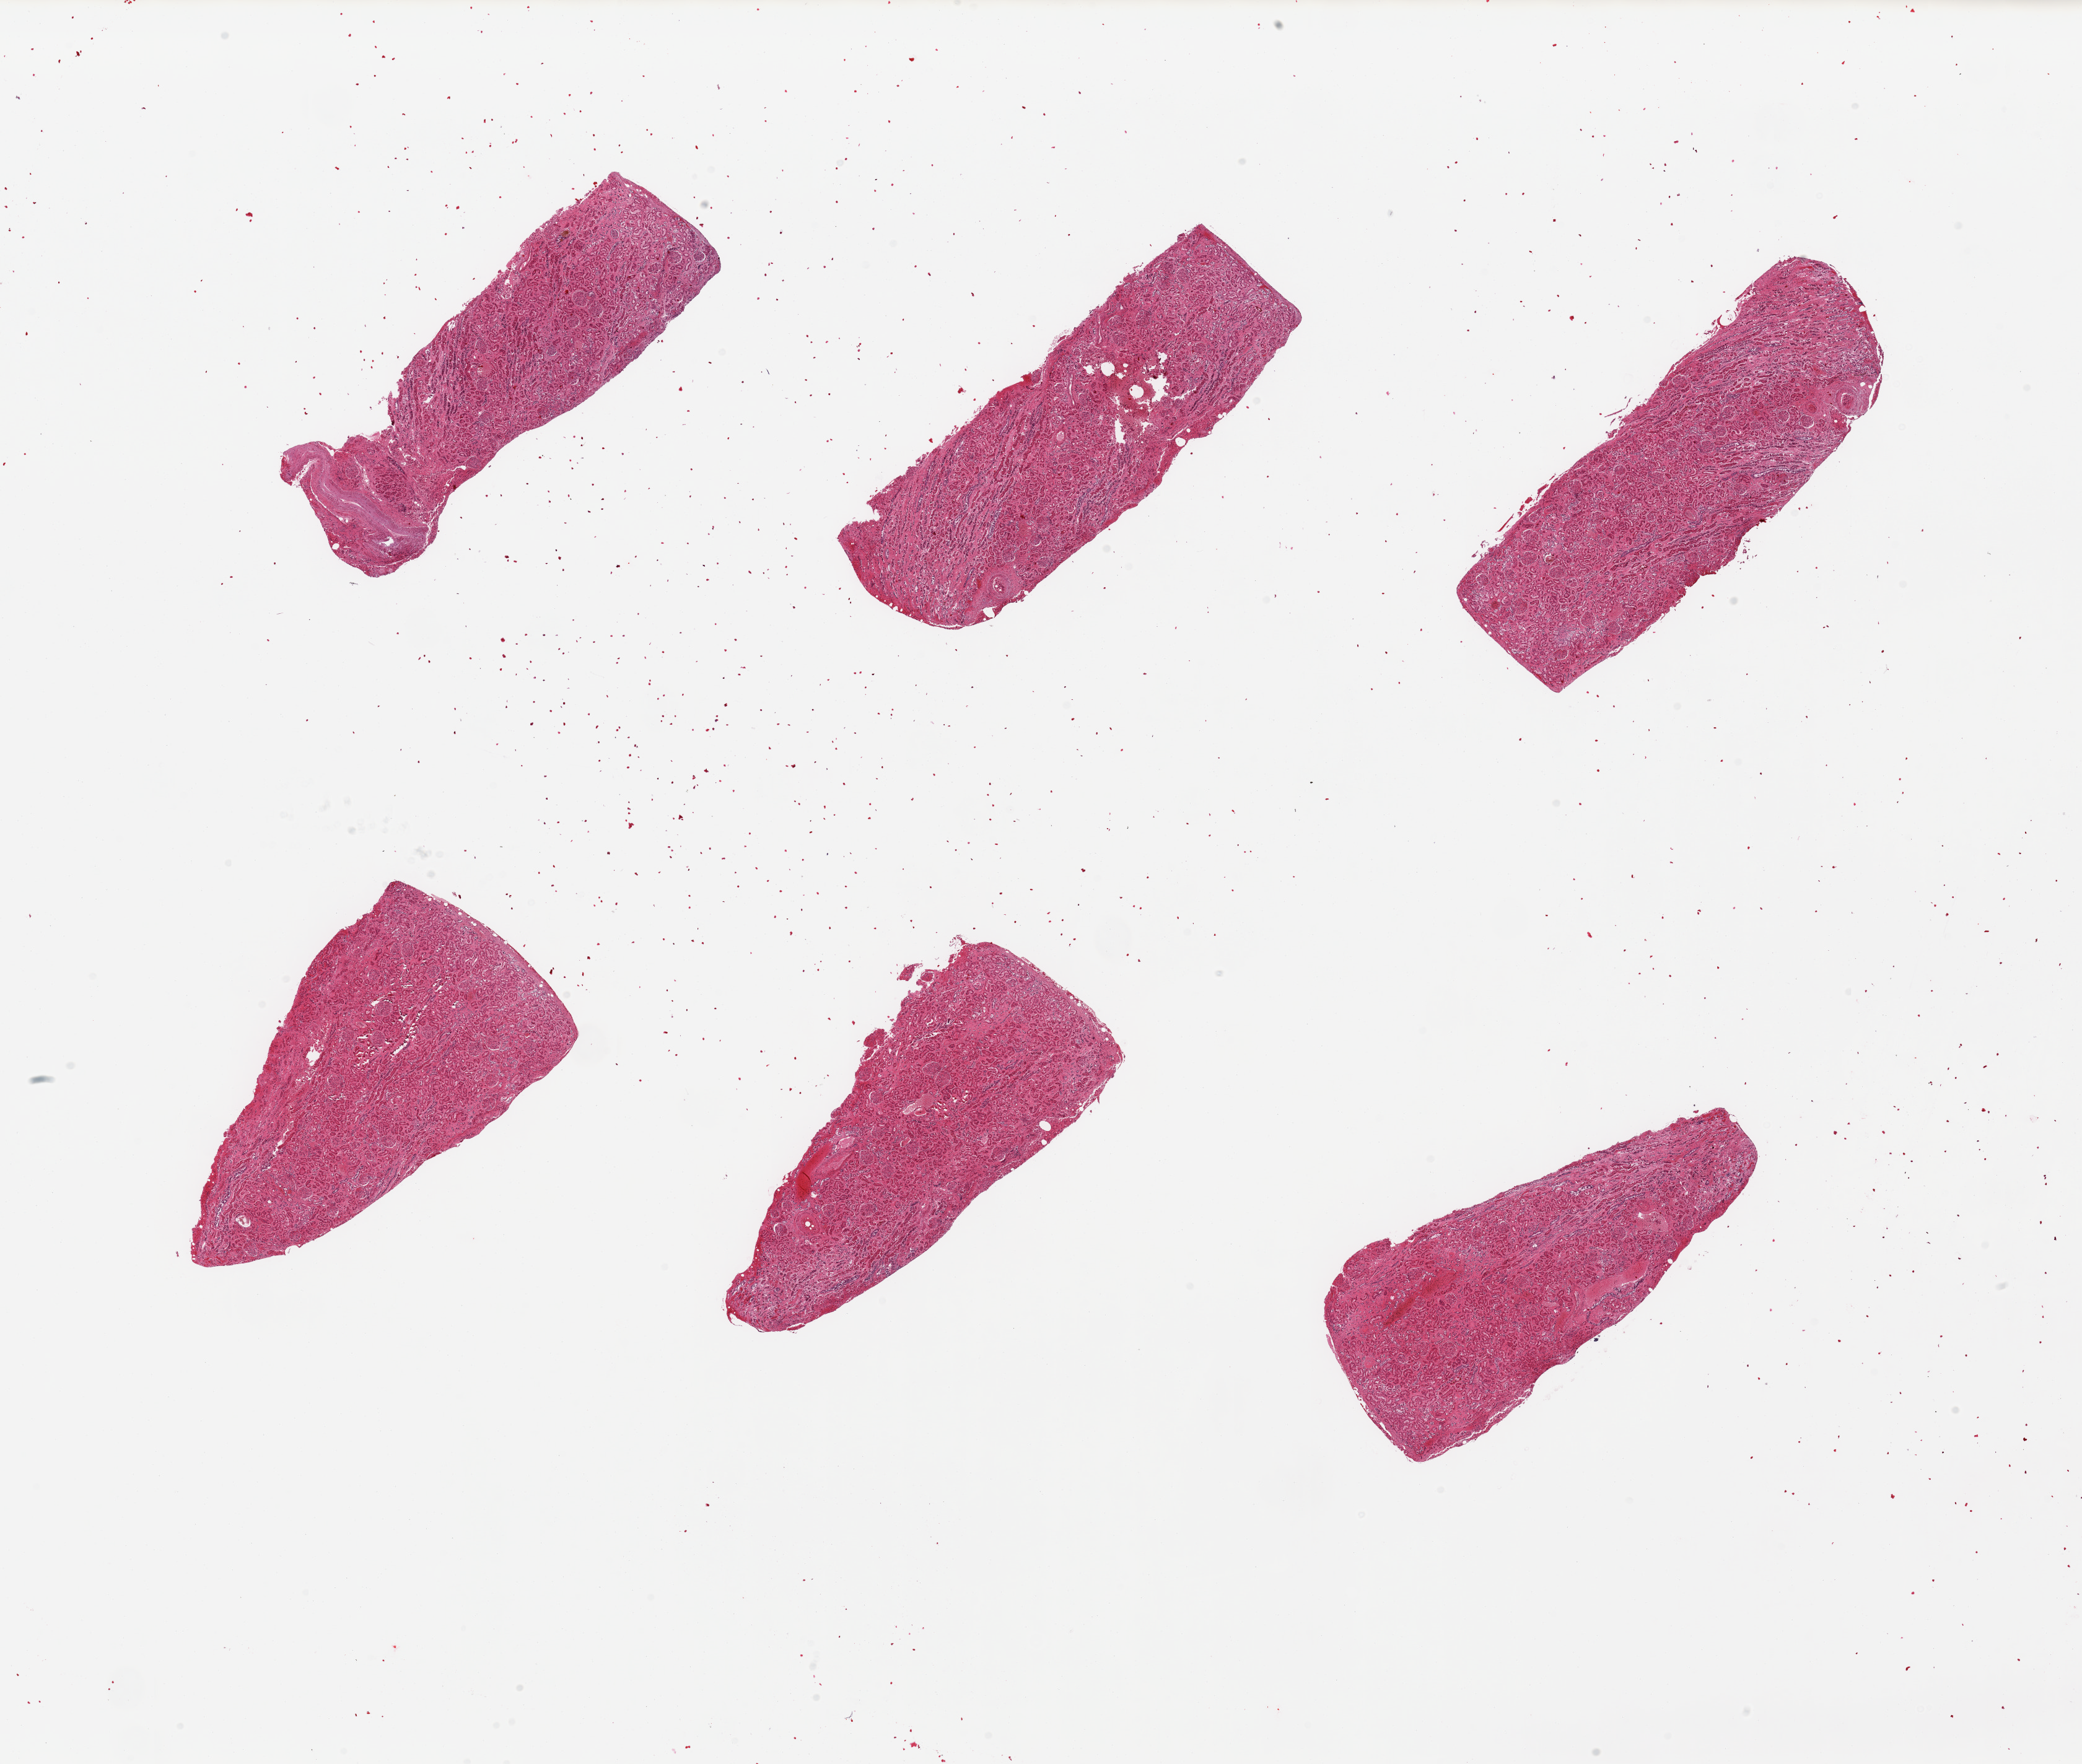
Digitized hematoxylin and eosin (H&E)-stained section, whole scanned area (about 26.6 x 22.5 mm, from a 20x scan) shown as a low-resolution overview; PAXgene-fixed paraffin-embedded (PFPE) section; sampled site (target tissue): renal cortex; donor tissue sample. Donor: male.
Pathologist's review note for this sample: 6 pieces; mild arterio and arteriolonephrosclerosis; congestion.